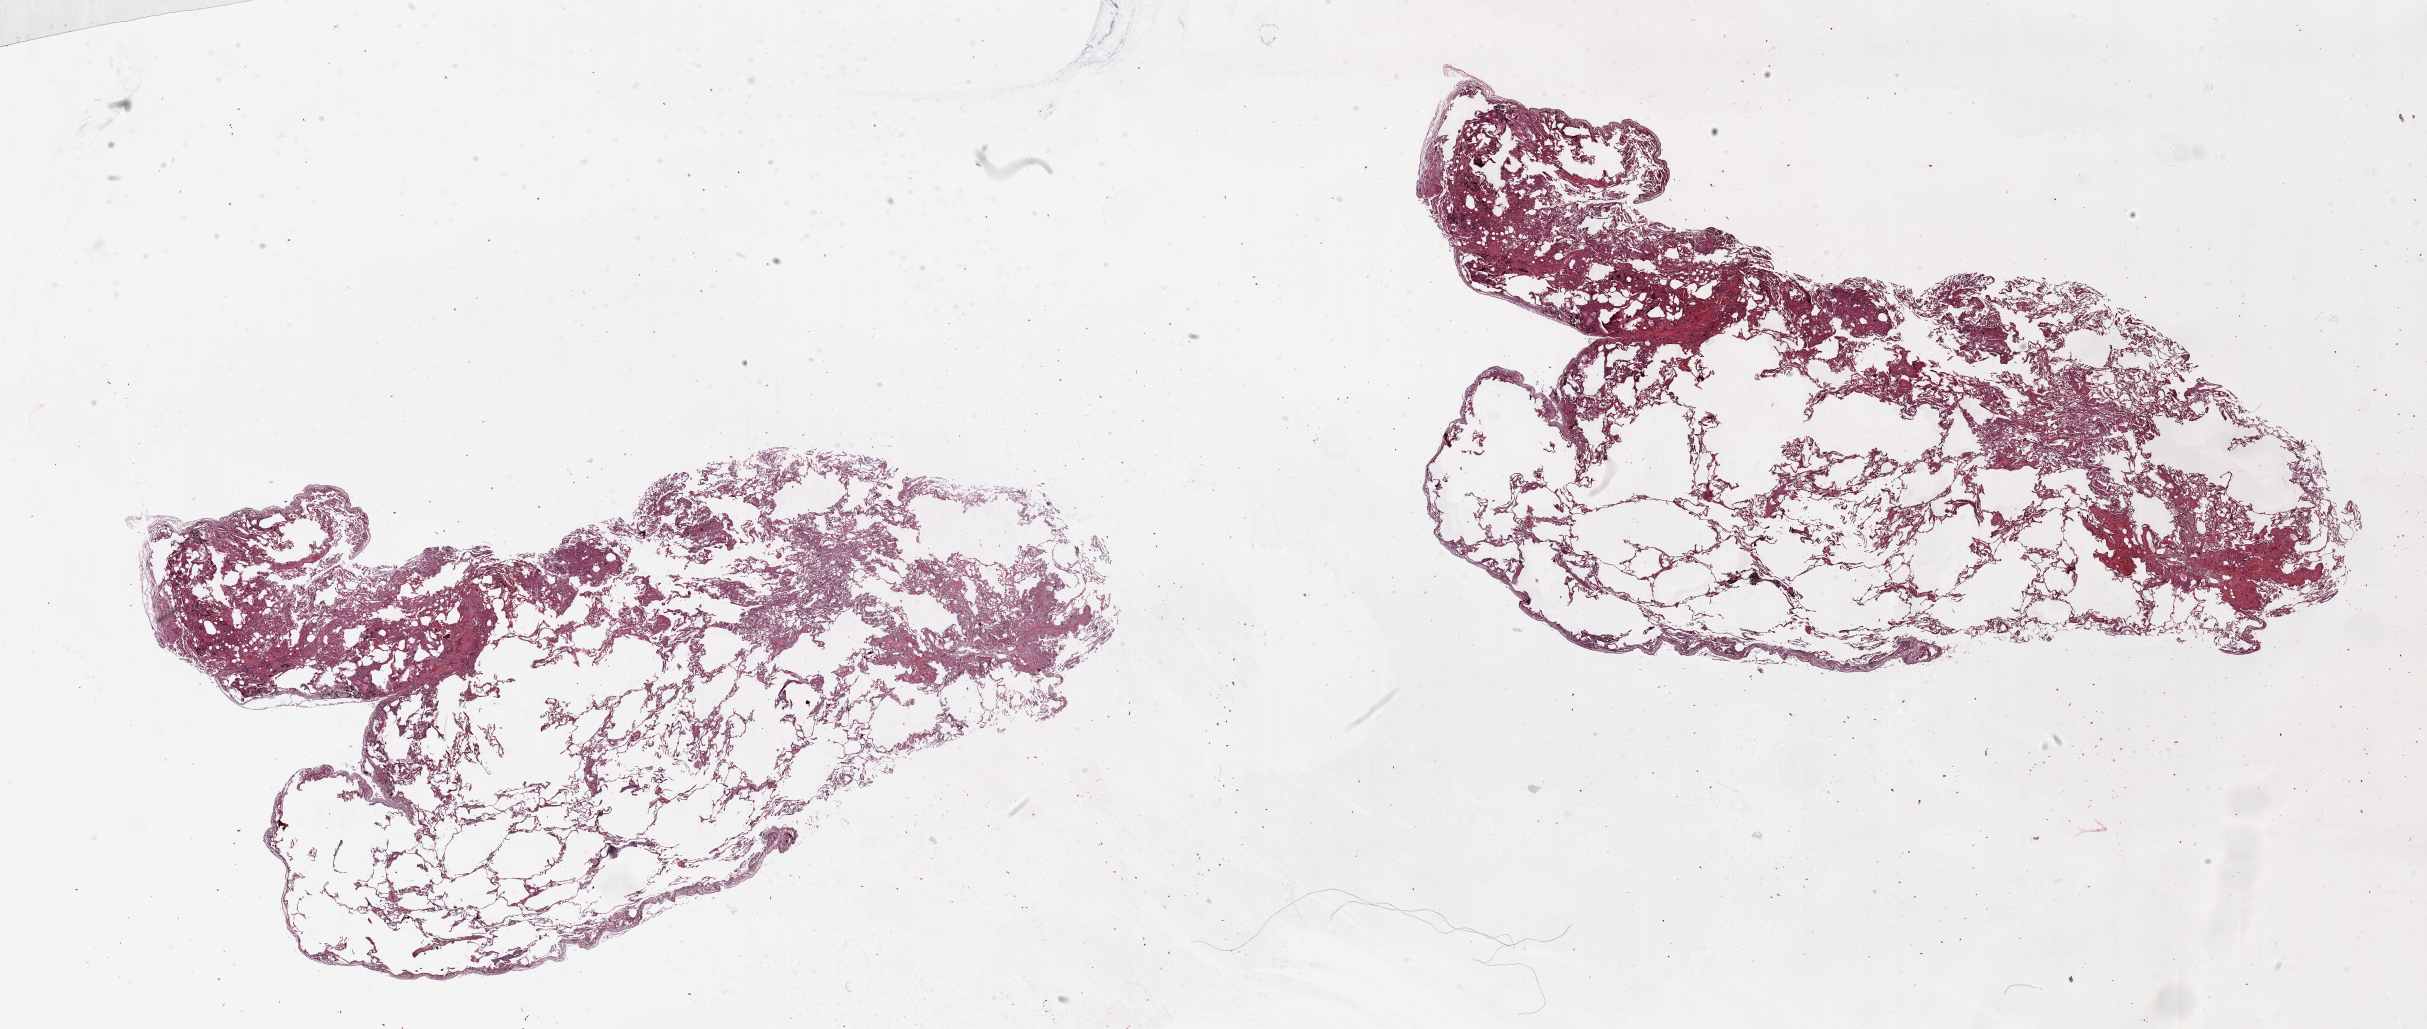
Whole-slide histology image, Hematoxylin and eosin (H&E) stained — shown as a low-resolution overview of the whole scanned area (about 38.4 x 16.3 mm, from a 20x scan), normal (non-tumour) tissue sample, lung. 56-year-old male patient.
• this section: normal (non-tumour) tissue from the same patient
• patient diagnosis: Adenocarcinoma, NOS